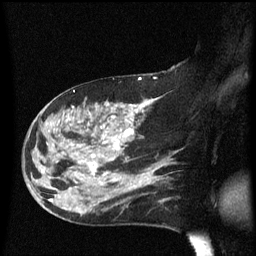
Breast MRI (dynamic contrast-enhanced), one sagittal slice. Dynamic contrast-enhanced series, image 2 of 3 at this slice position (ordered by acquisition). 1.5 T. TE 4.2 ms, TR 8.4 ms. 2.2 mm slice thickness. 256 × 256 image matrix, field of view 200 × 200 mm. Patient: female, 47 years.
Outlined on this slice (semi-automatically segmented with operator editing):
- analysis volume of interest (the breast-tissue region the enhancement analysis was run in; not a lesion): bounding box [x1, y1, x2, y2] px = [24, 97, 149, 206]
- tumour enhancement mask (voxels above the 70 % enhancement threshold inside the analysis volume of interest): [50, 101, 149, 203]